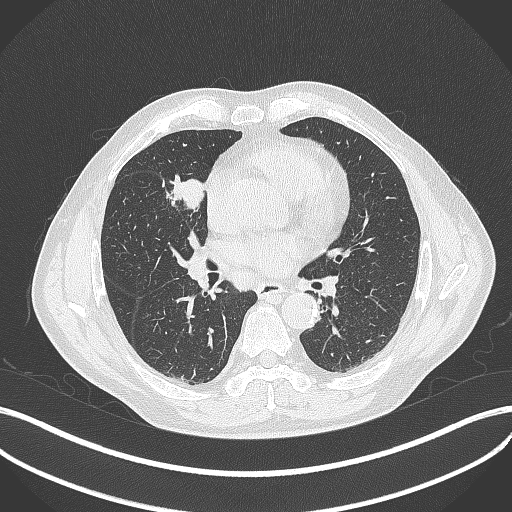
Chest CT, one axial slice. Position 200 of 429 along the scan axis. Reconstruction kernel B70f. Lung window (W 1500 / L -600 HU). 512 × 512 image matrix, field of view 400 × 400 mm. Male patient, age 61 years. From the clinical record (not read from this slice): clinical TNM (as recorded): T2b N1 M0.
Annotated regions visible in this slice (rectangle marked by the reading radiologist):
- lung tumour (recorded histology: squamous cell carcinoma): bounding box <169,172,212,215> (left, top, right, bottom; pixels)